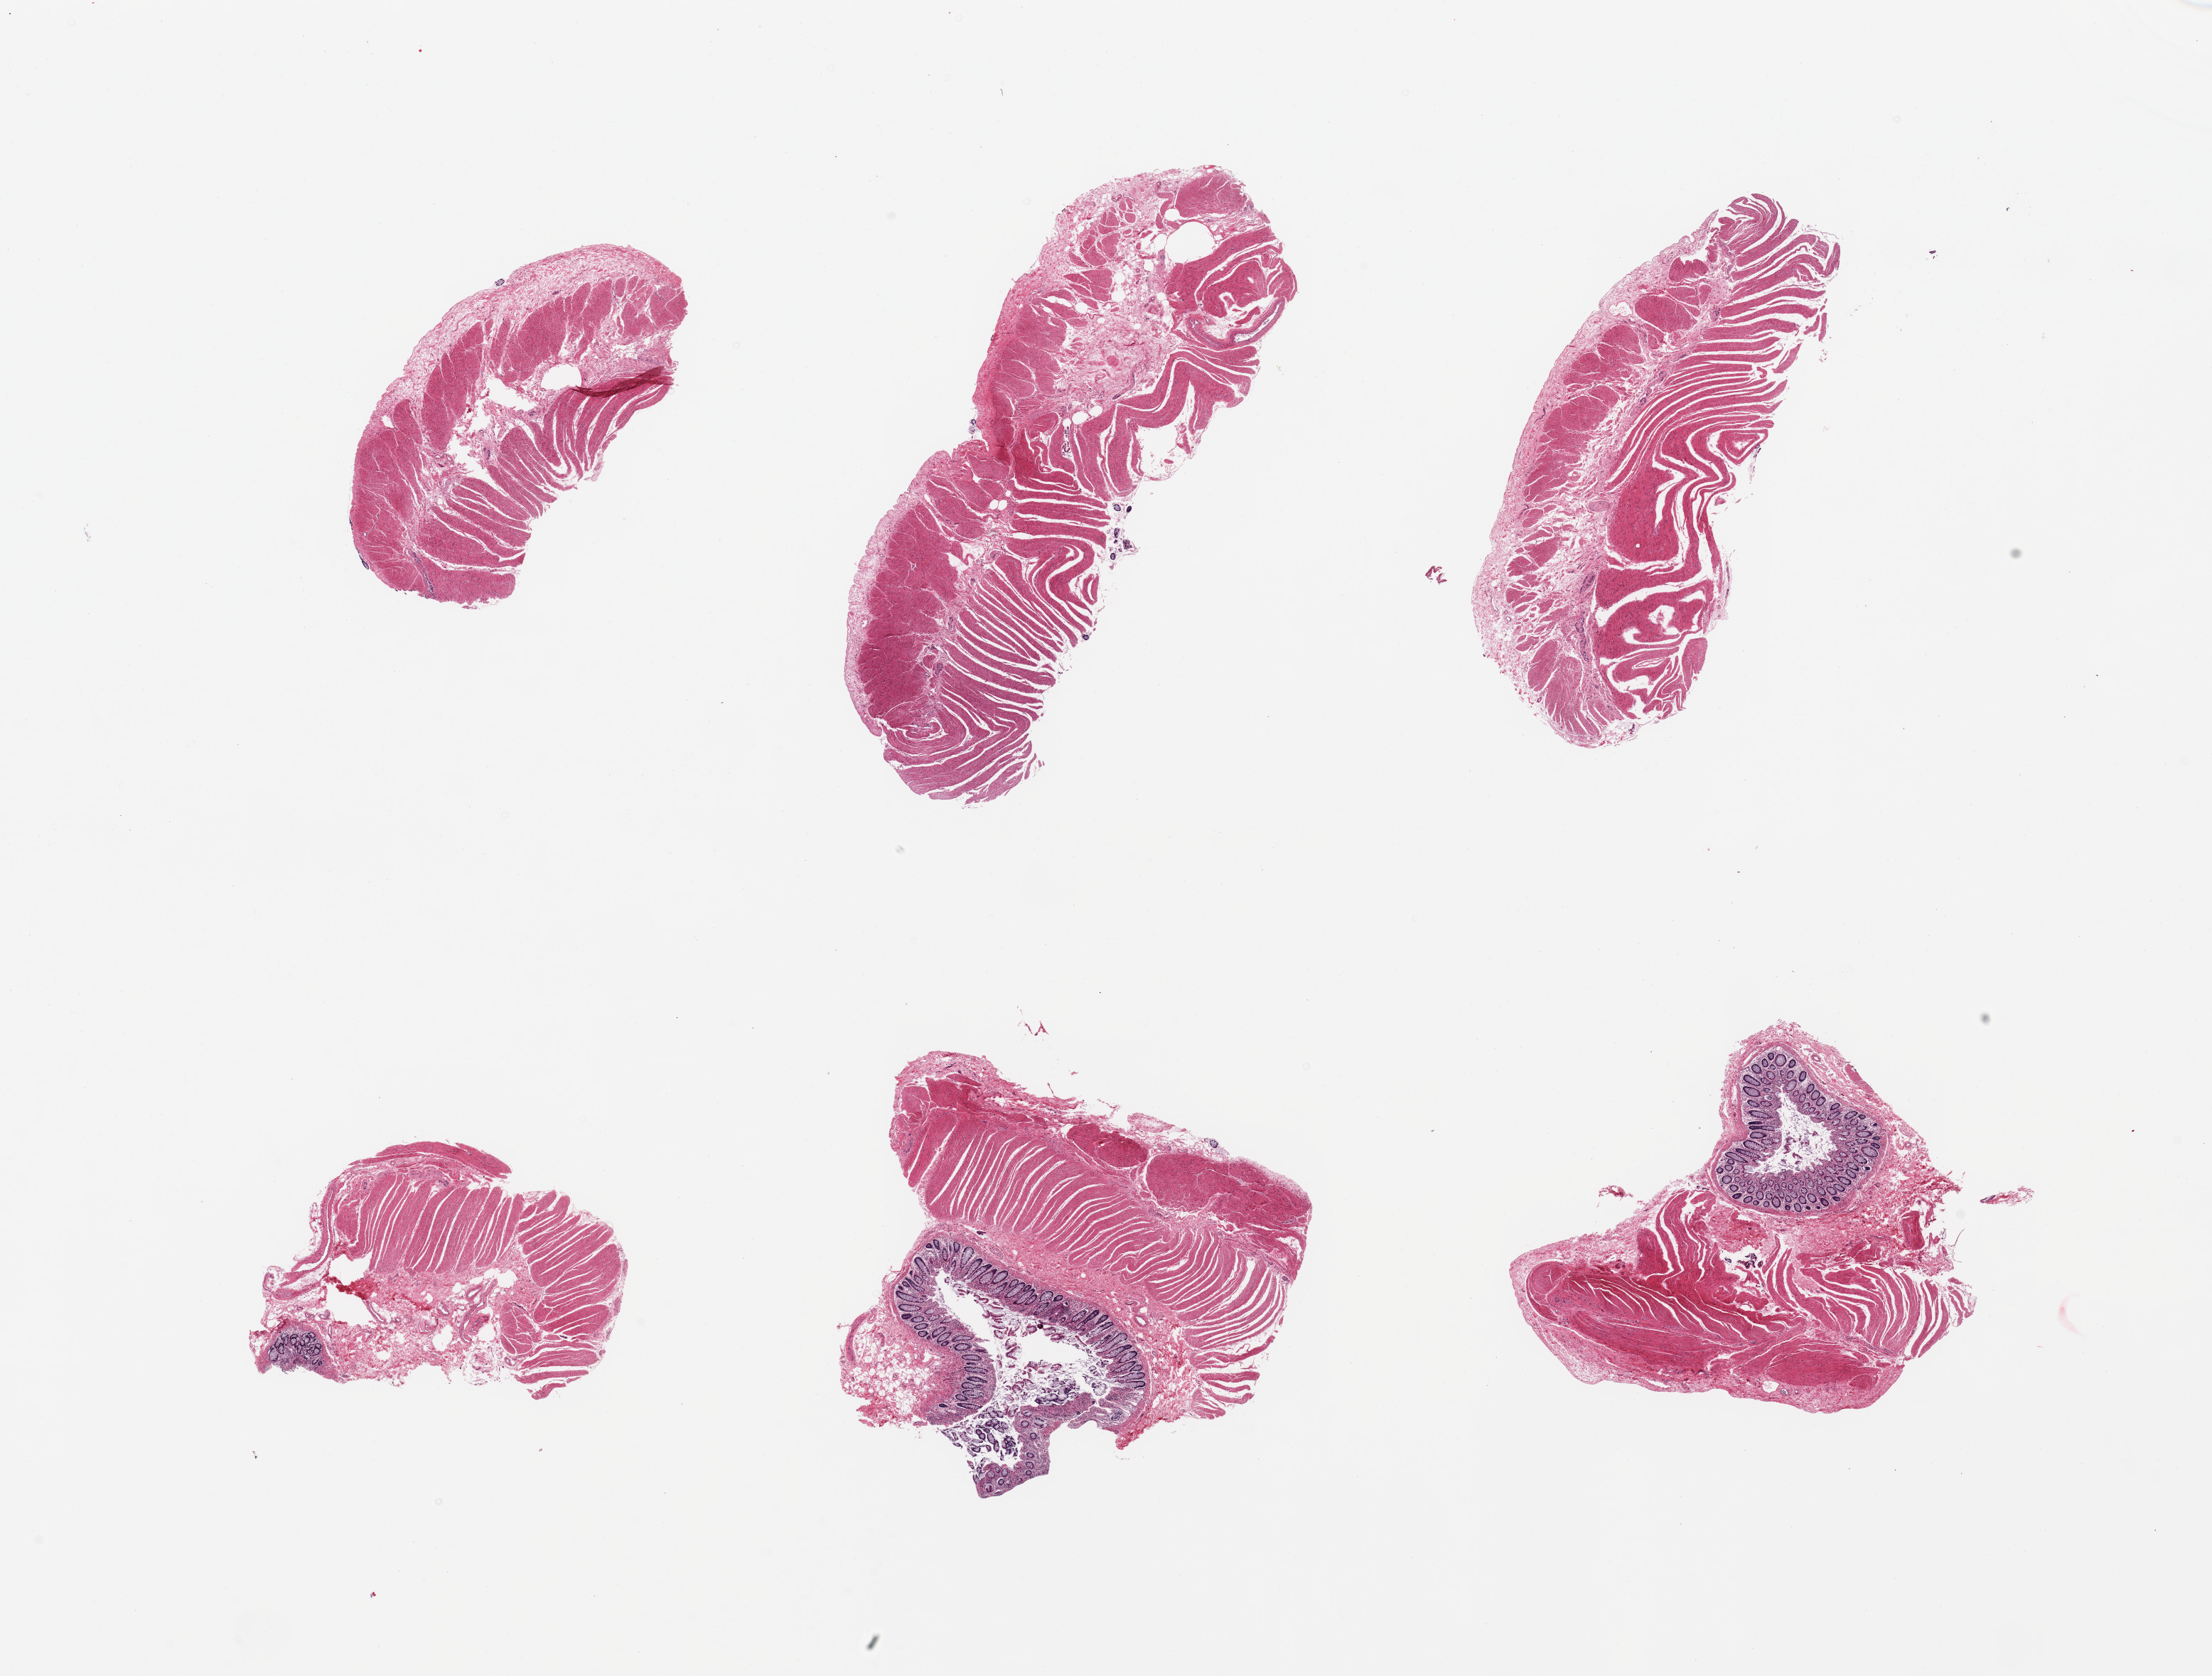
H&E whole-slide image — a low-resolution overview of the entire scanned area, about 24.6 x 18.6 mm (from a 20x scan). PAXgene-fixed paraffin-embedded (PFPE) section. Section of sigmoid colon (target tissue). Tissue donor sample. Donor sex: male.
• pathologist's review note for this sample: 6 pieces; predominantly muscularis, but 3 of 6 pieces include colonic mucosa